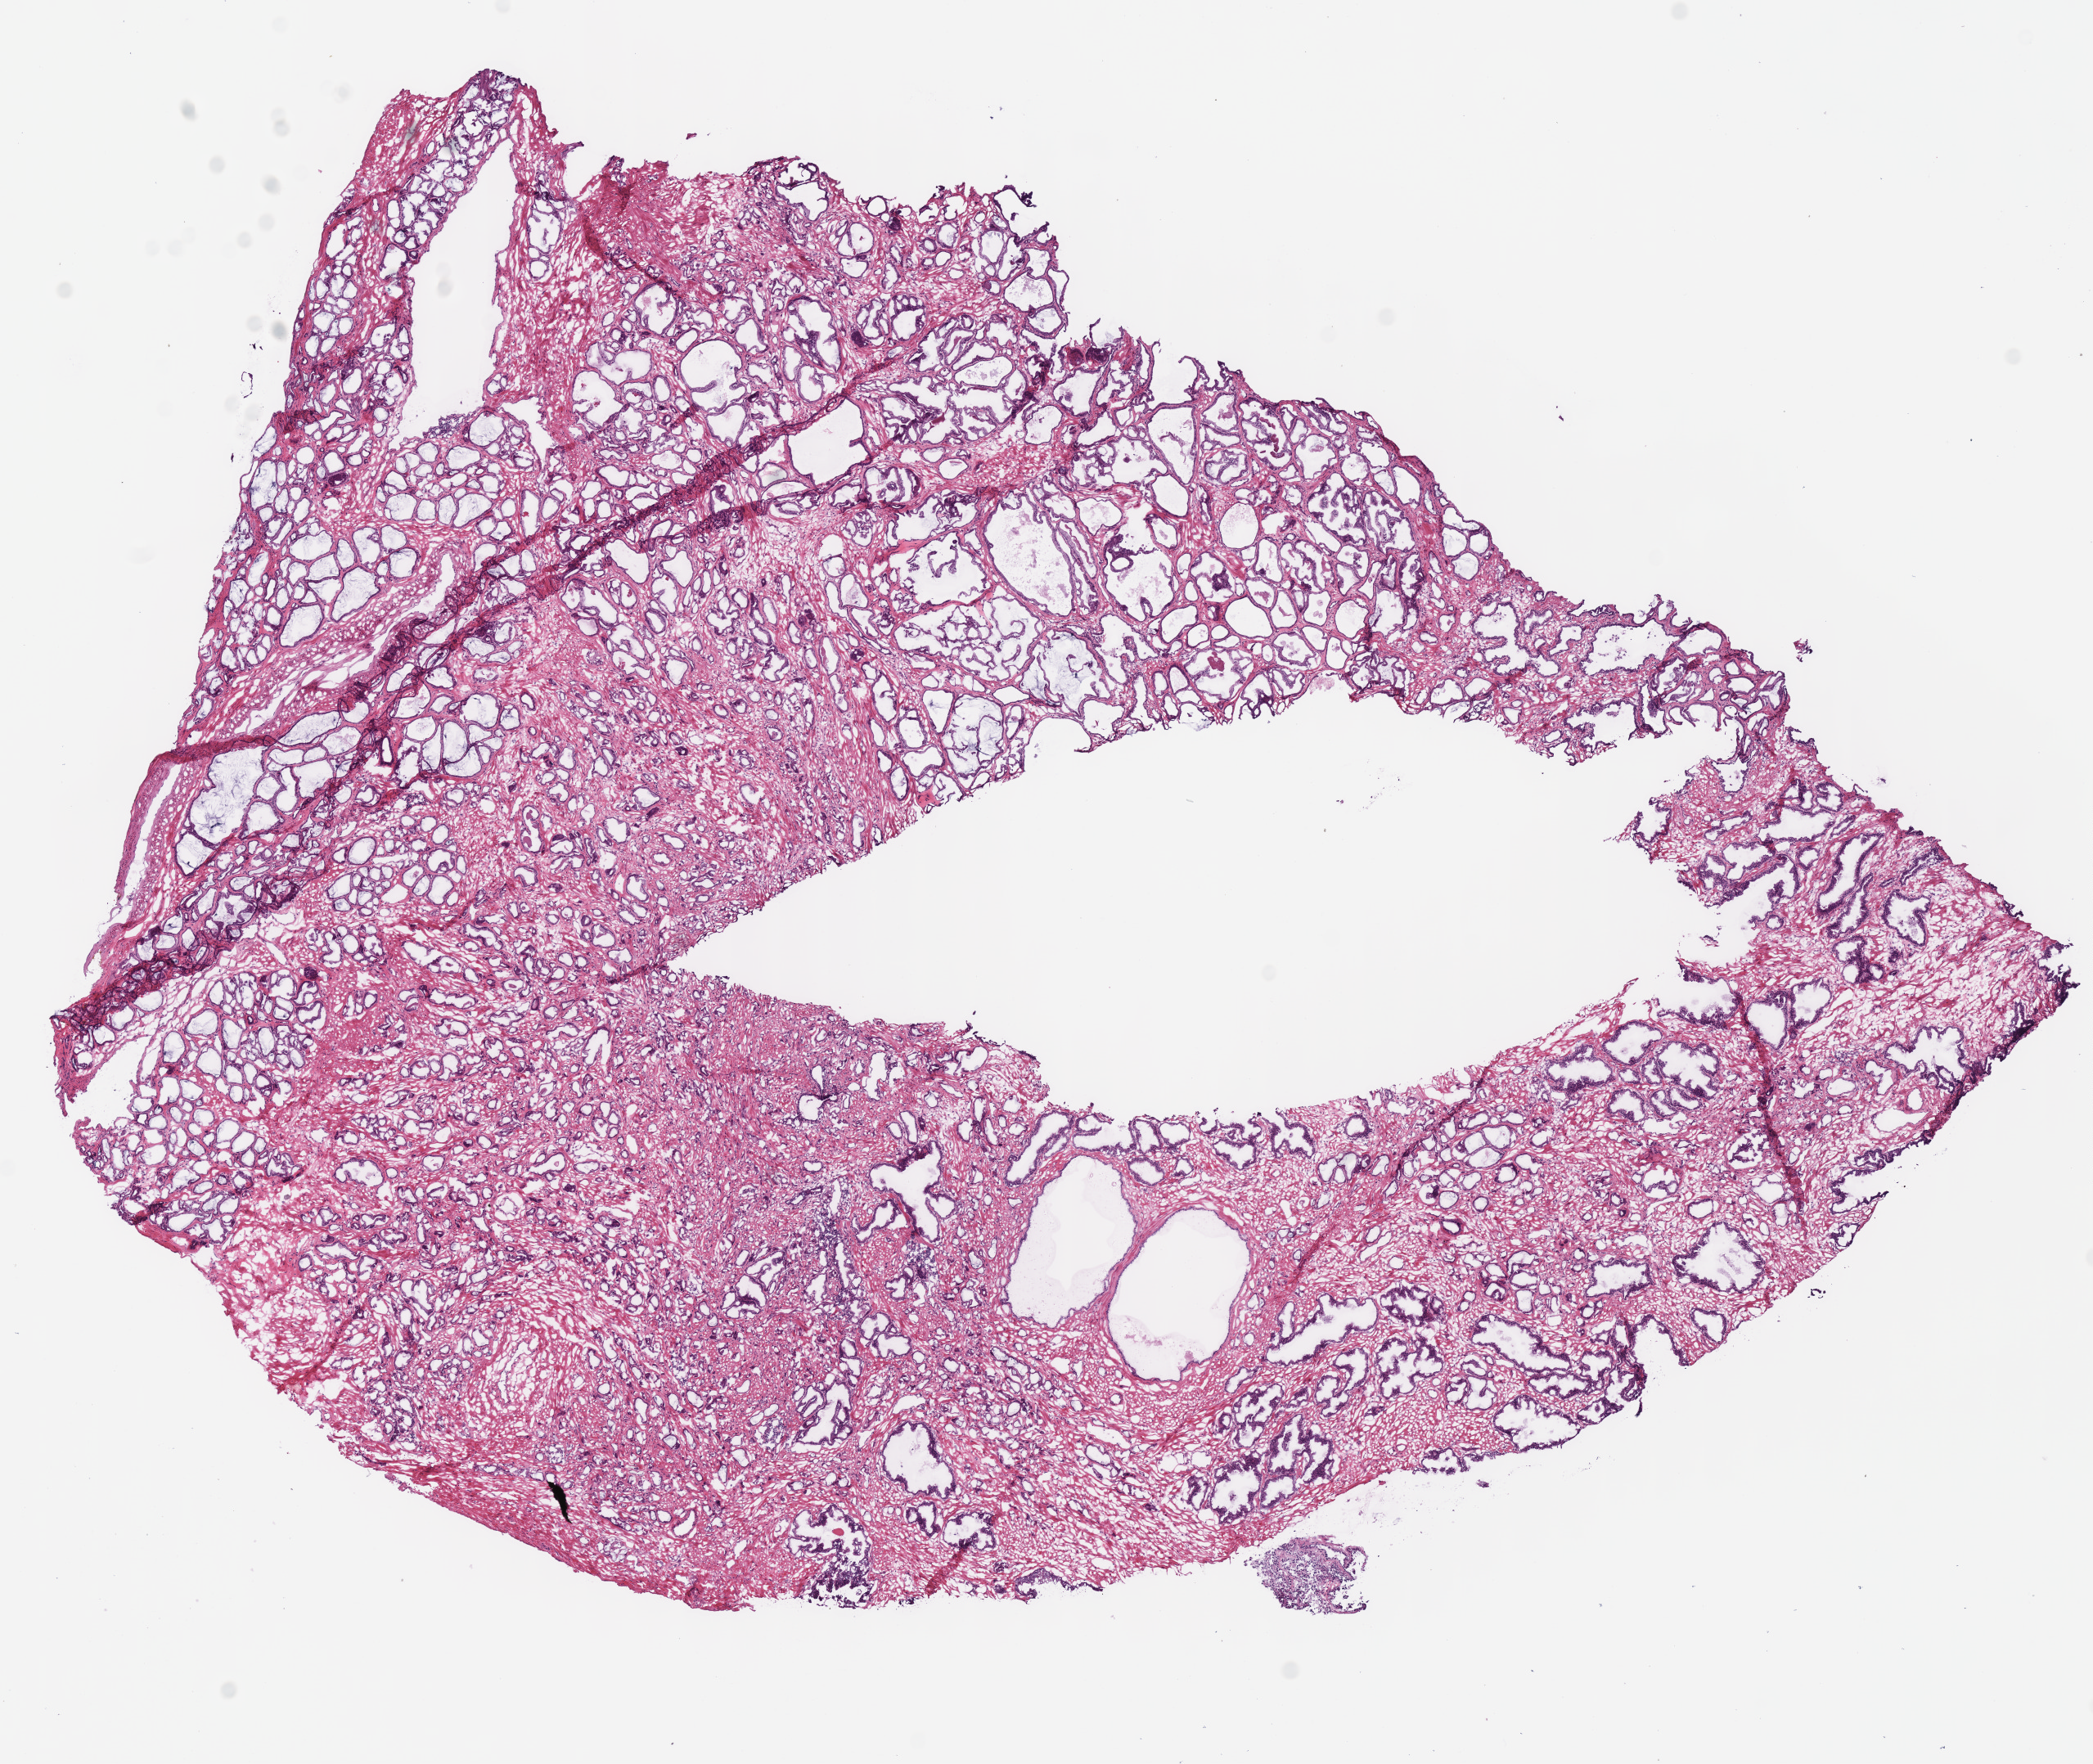
Digitized H&E-stained tissue section (whole slide), shown as a low-resolution overview of the whole scanned area (about 10.1 x 8.5 mm, acquisition: 40x scan). Frozen section. Prostate, primary tumour sample. Patient: male, age at initial diagnosis 49 years. Gleason score: 7 (3+4). Slide review estimates, as recorded: tumour cells 50%, tumour nuclei 50%, normal cells 30%, stromal cells 20%, necrosis 0%.
• diagnosis: Acinar cell carcinoma (prostate gland)
• laterality: bilateral